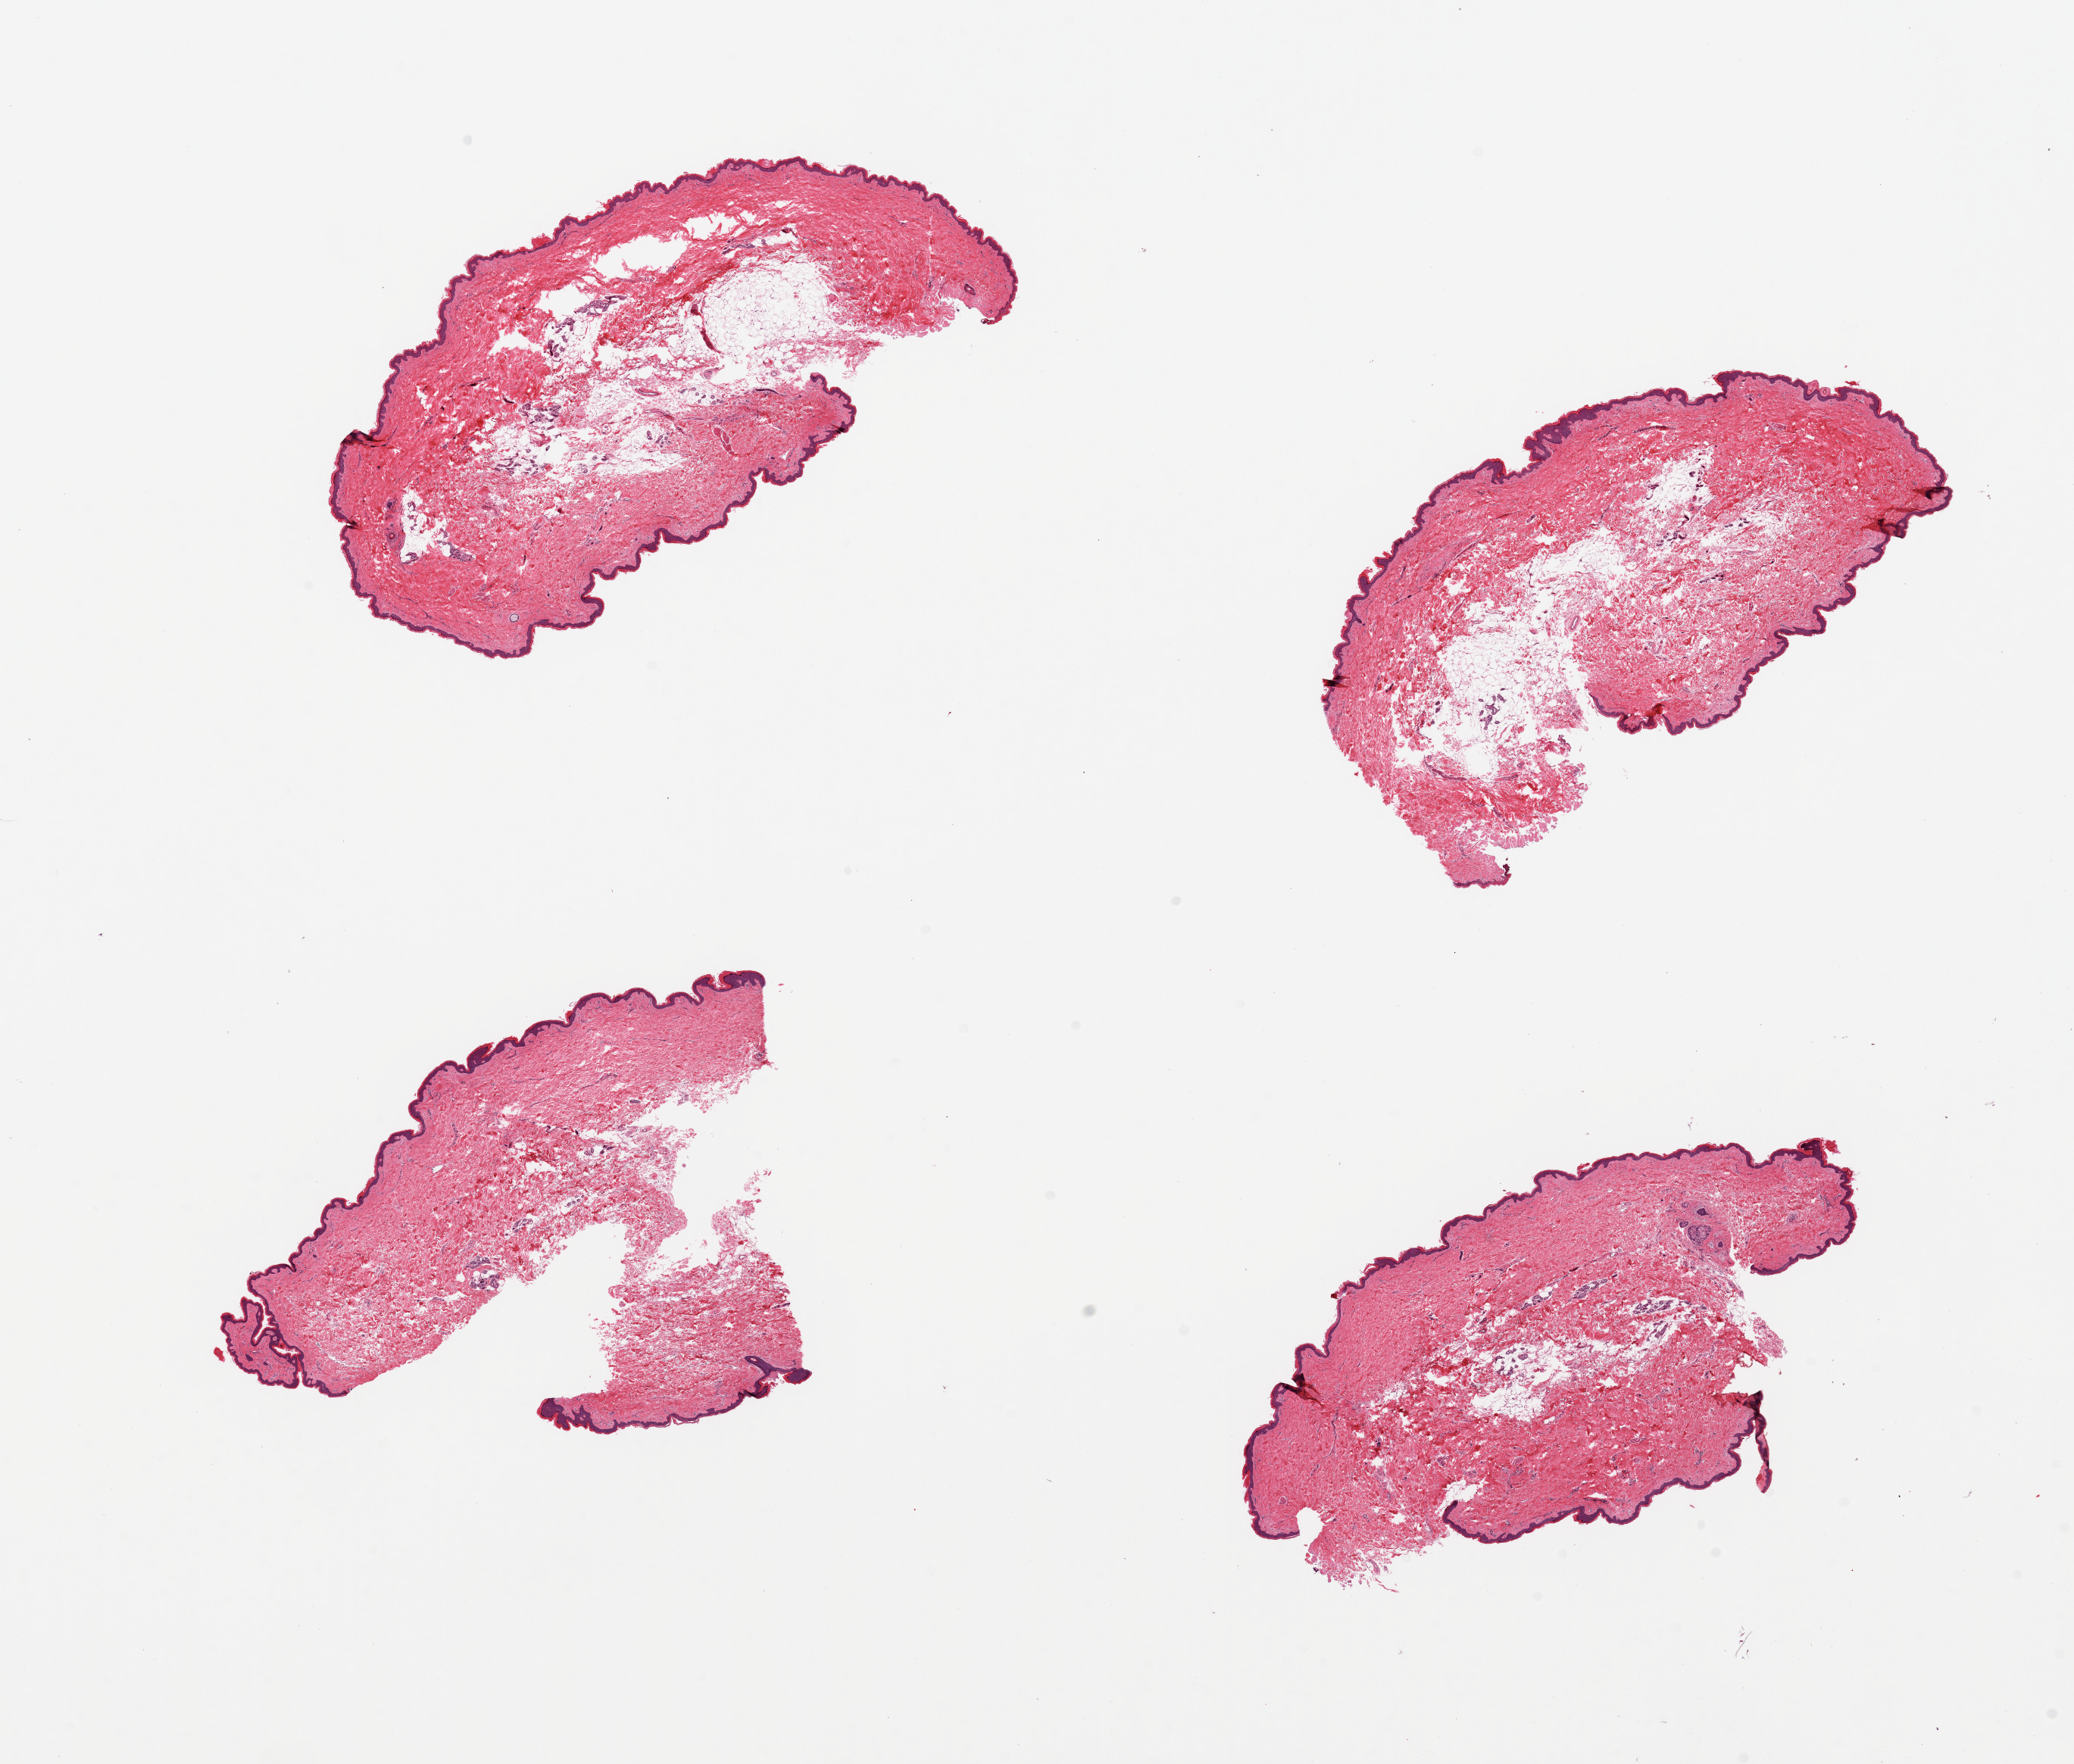
Whole-slide image, hematoxylin and eosin (H&E) stain — a low-resolution overview of the entire scanned area, about 21.7 x 18.4 mm (acquisition: 20x scan); PAXgene-fixed paraffin-embedded (PFPE) section; section of skin of suprapubic region (target tissue); tissue donor sample.
Pathologist's review note for this sample: 4 pieces.